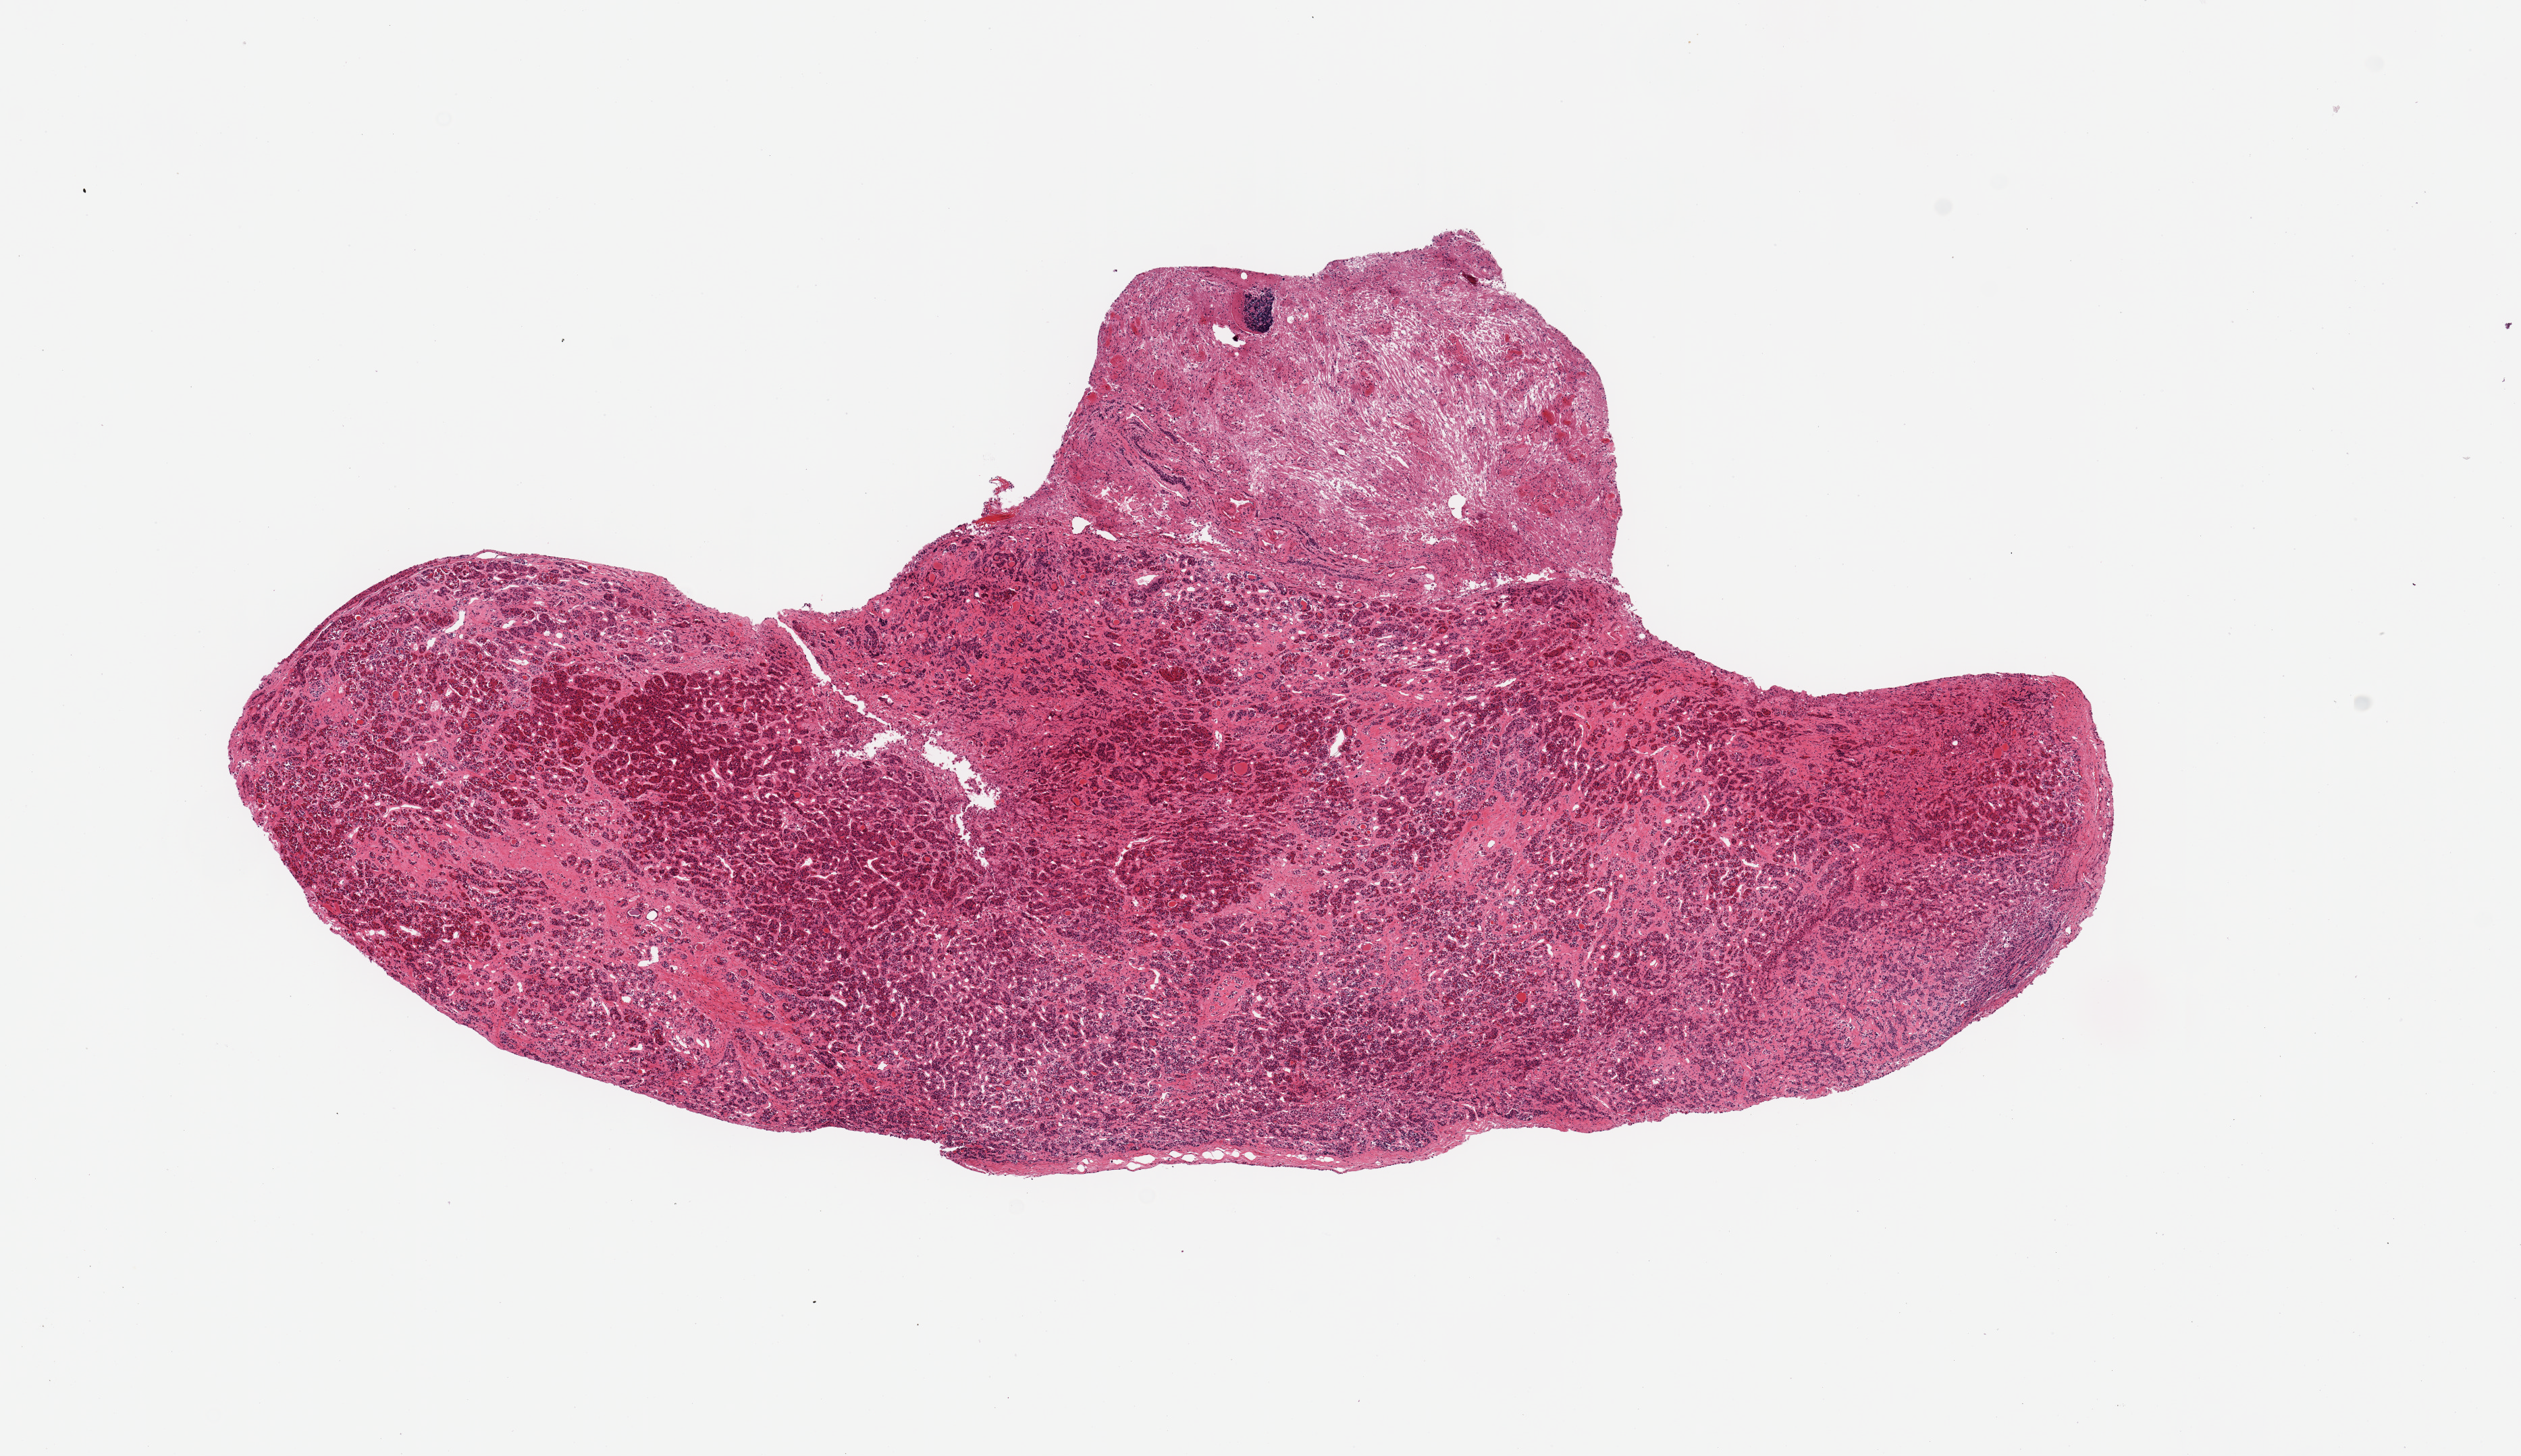
Digitized H&E-stained section — shown as a low-resolution overview of the whole scanned area (about 14.8 x 8.5 mm), PAXgene-fixed paraffin-embedded (PFPE) section, sampled site (target tissue): pituitary, donor tissue sample. Donor: male.
• pathologist's review note for this sample: 1 piece; good cross-section; interstitial fibrosis in anterior lobe with 20% fibrous content; neurohypophysis